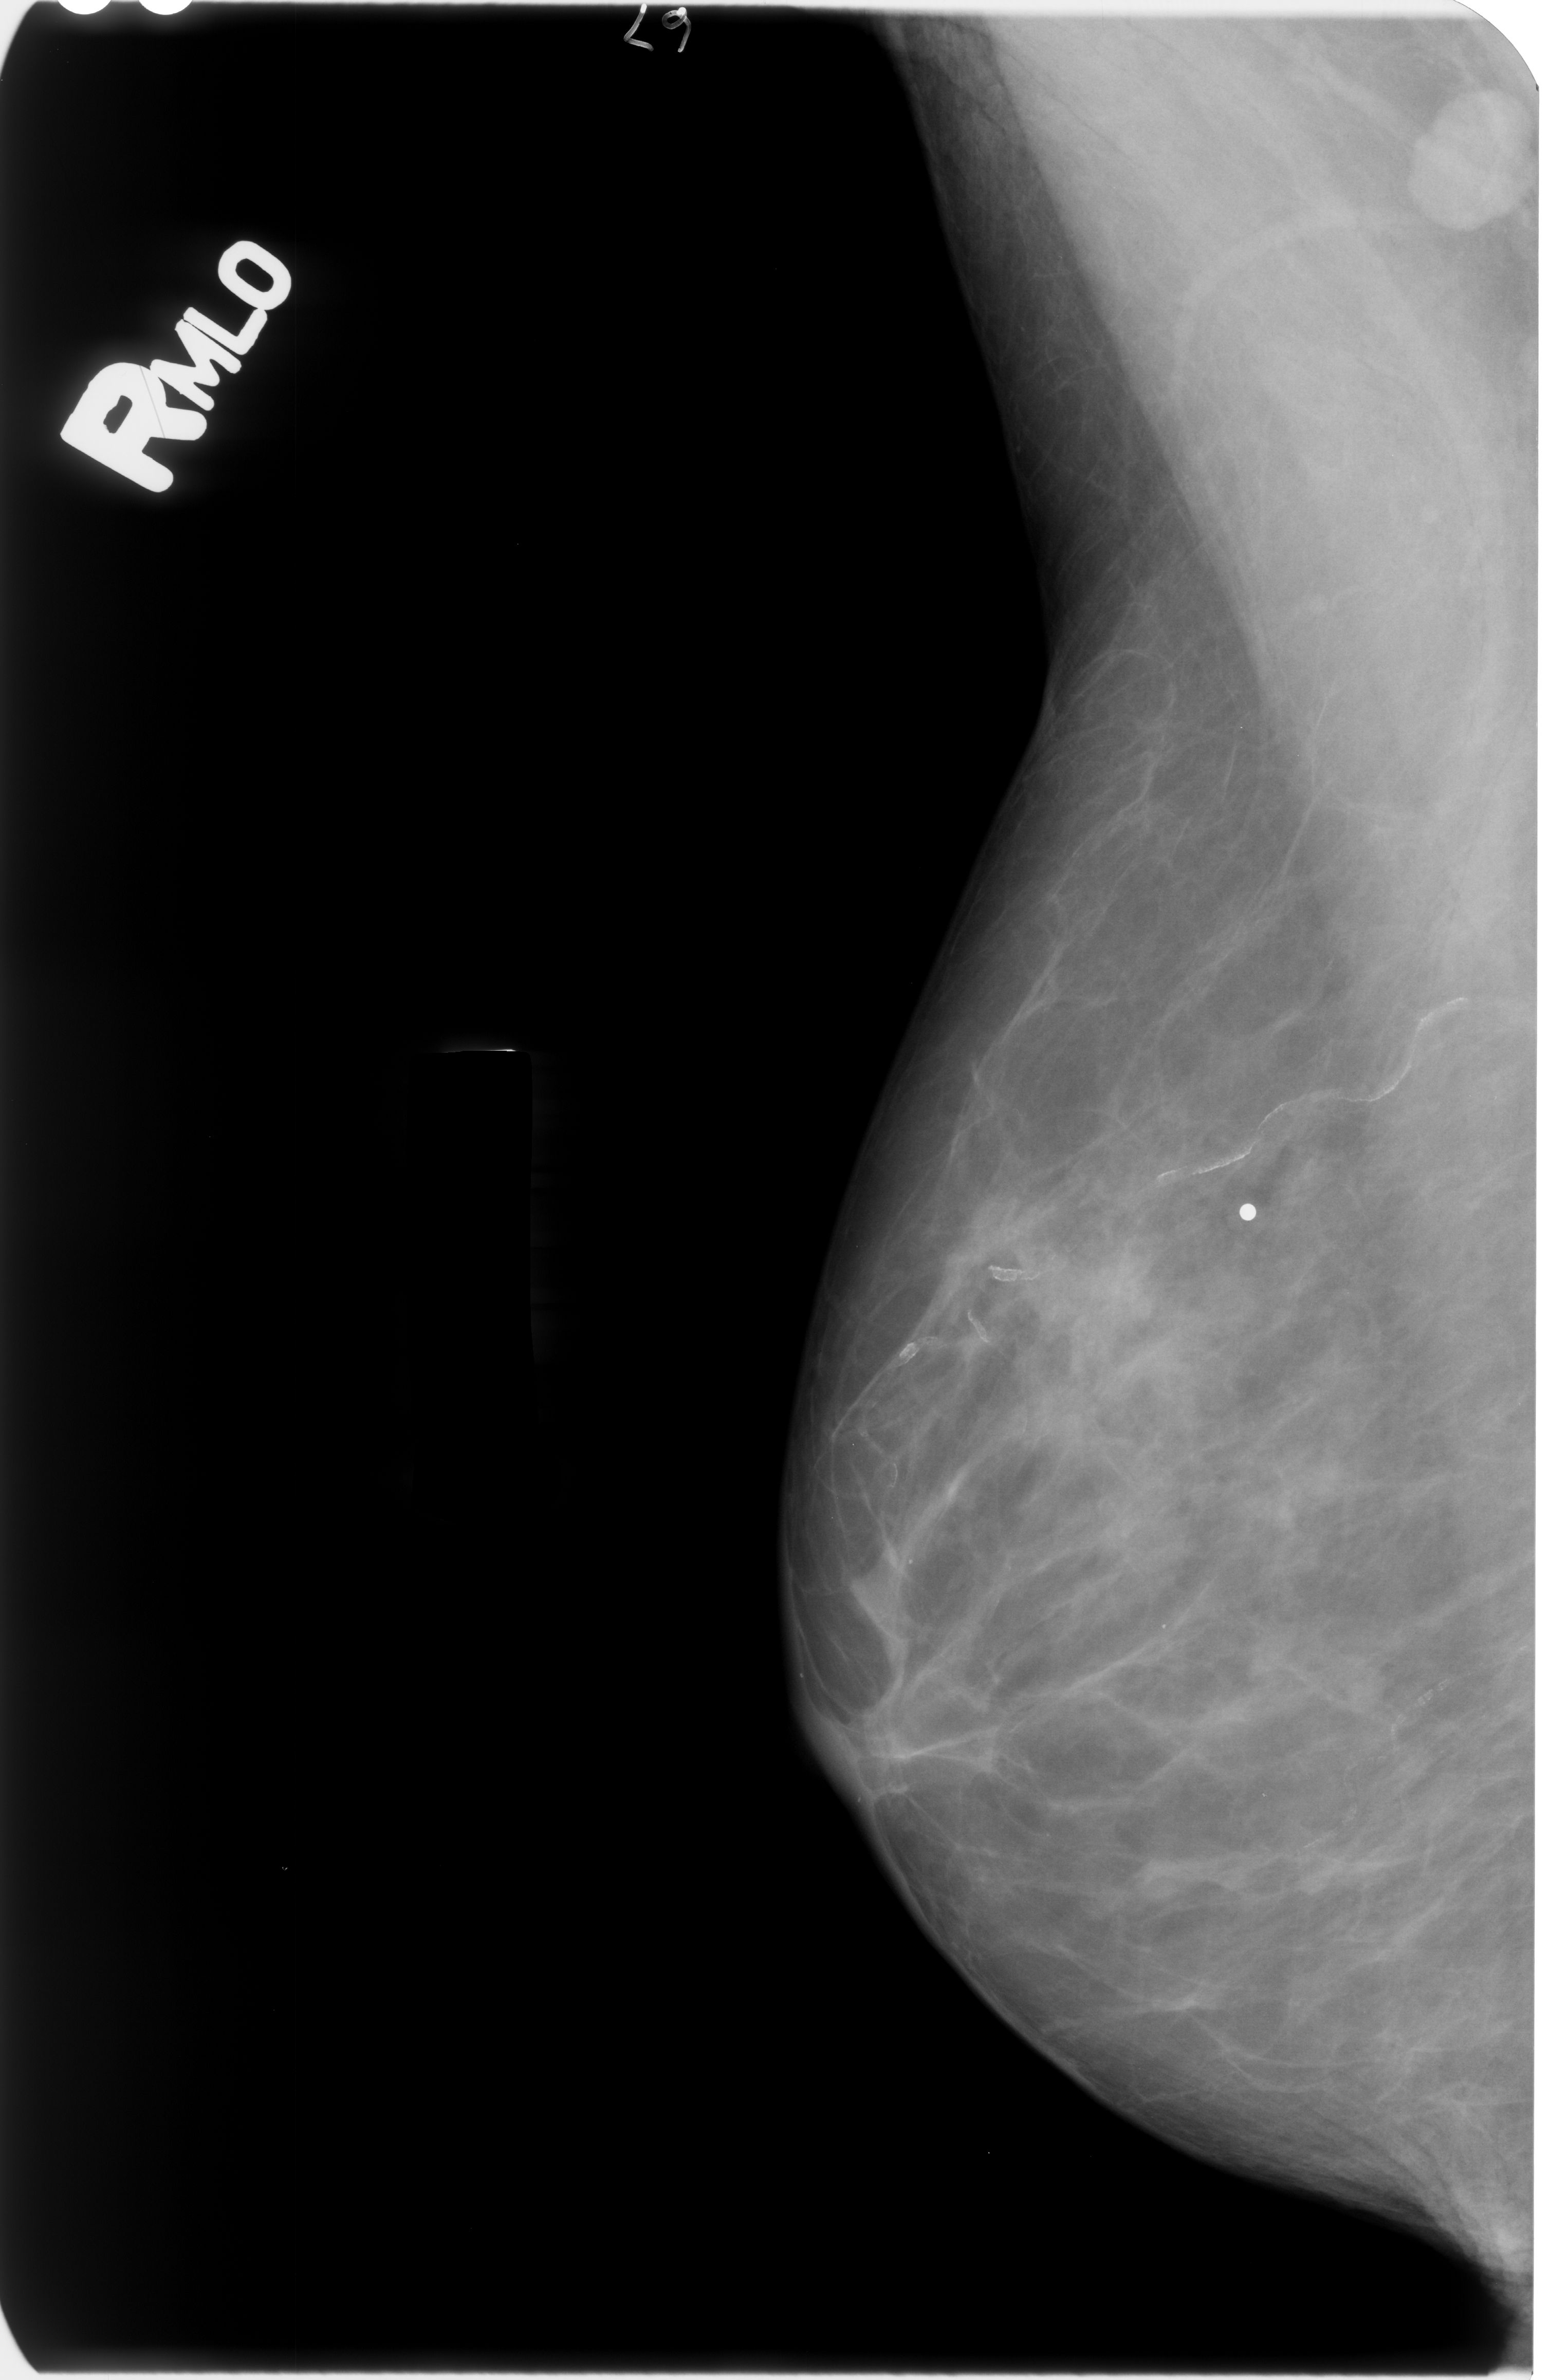
Mammogram (digitized film); right breast; mediolateral oblique (MLO) view; BI-RADS breast density category 2 (scale 1–4); 1550 × 2380 image matrix.
Expert-marked regions of interest on this image (one box per marked abnormality):
- calcifications, morphology vascular; BI-RADS assessment category 2; subtlety rating 4 on a 1 (subtle) to 5 (obvious) scale; outcome (as recorded, no biopsy): benign without callback (not worked up further): bounding box (x1, y1, x2, y2) in pixels: (838, 986, 1489, 1415)